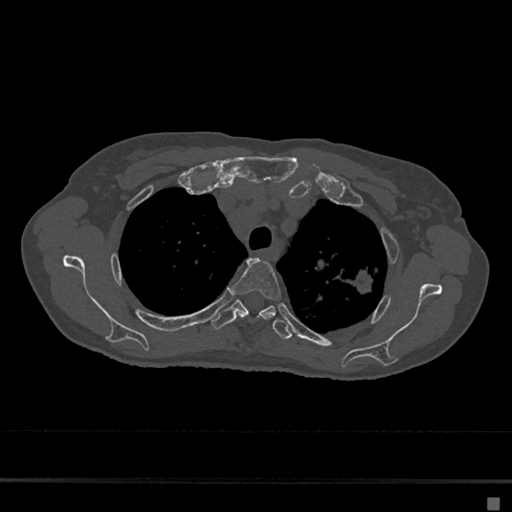
CT including the spine, one axial slice; slice 524 of 797 in the series (ordered by position); reconstruction kernel Br40s/3; bone window (W 1800 / L 400 HU); 0.5 mm slice thickness; 512 × 512 image matrix. Female patient, age 68 years. From the clinical record (not read from this slice): primary cancer: renal.
Outlined on this slice (semi-automatically segmented with operator editing):
- T3 vertebra: bounding box [x1, y1, x2, y2] px = [231, 259, 281, 320]
- T4 vertebra: [210, 299, 291, 340]